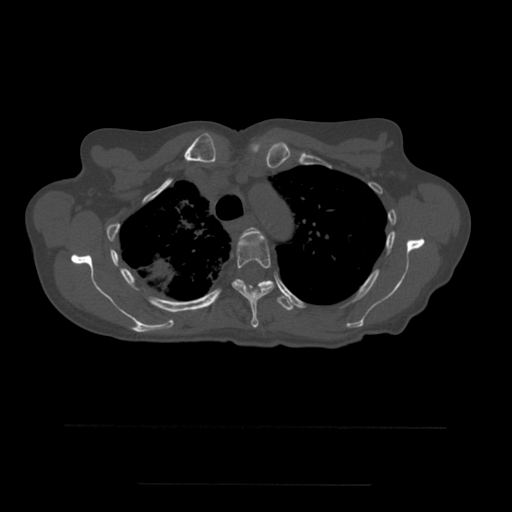
CT including the spine, one axial slice; slice 405 of 544 in the series (ordered by position); bone window (W 1800 / L 400 HU); 1.25 mm slice thickness; 512 × 512 image matrix, field of view 350 × 350 mm. Patient age 58 years. From the clinical record (not read from this slice): primary cancer: lung.
Annotated regions visible in this slice (semi-automatic segmentation, software-assisted and operator-edited):
- T3 vertebra: bounding box [x1, y1, x2, y2] px = [240, 227, 265, 241]
- T4 vertebra: [232, 235, 274, 328]
- T5 vertebra: [220, 279, 295, 311]